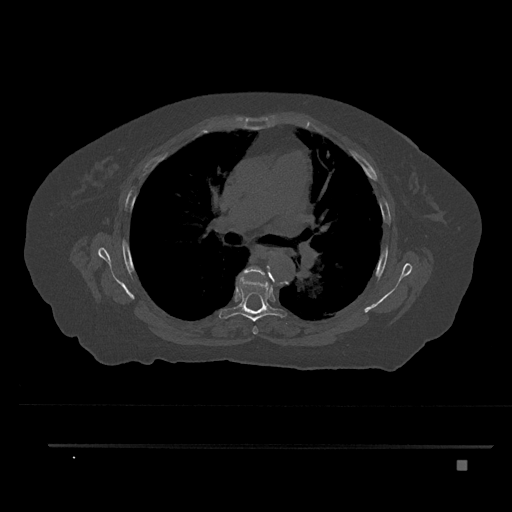
CT including the spine, one axial slice. Slice 535 of 797 in the series (ordered by position). Reconstruction kernel Br40s/3. Bone window (W 1800 / L 400 HU). 0.5 mm slice thickness. 512 × 512 image matrix, field of view 437 × 437 mm. Female patient, age 76 years. Case-level facts recorded for this patient, not image findings: primary cancer: lung; vertebrae with lytic lesions (as recorded): T11, L3.
Outlined on this slice (semi-automatically segmented with operator editing):
- T5 vertebra: box from (x=237, y=266) to (x=268, y=335) px
- T6 vertebra: (x=219, y=274)–(x=287, y=321)